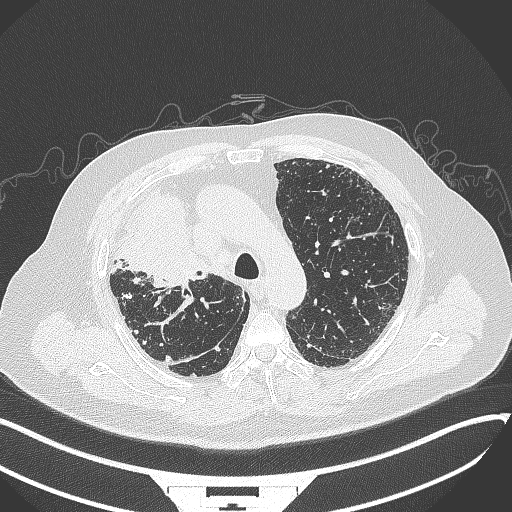
Chest CT, one axial slice. Slice 256 of 384 in the series (ordered by position). Lung window (W 1500 / L -600 HU). 1 mm slice thickness. 512 × 512 image matrix, field of view 400 × 400 mm. Male patient, age 69 years. From the clinical record (not read from this slice): clinical TNM (as recorded): T4 N3 M1.
Structures marked on this image (bounding box drawn by a radiologist):
- lung tumour (recorded histology: adenocarcinoma): box from (x=115, y=189) to (x=210, y=288) px